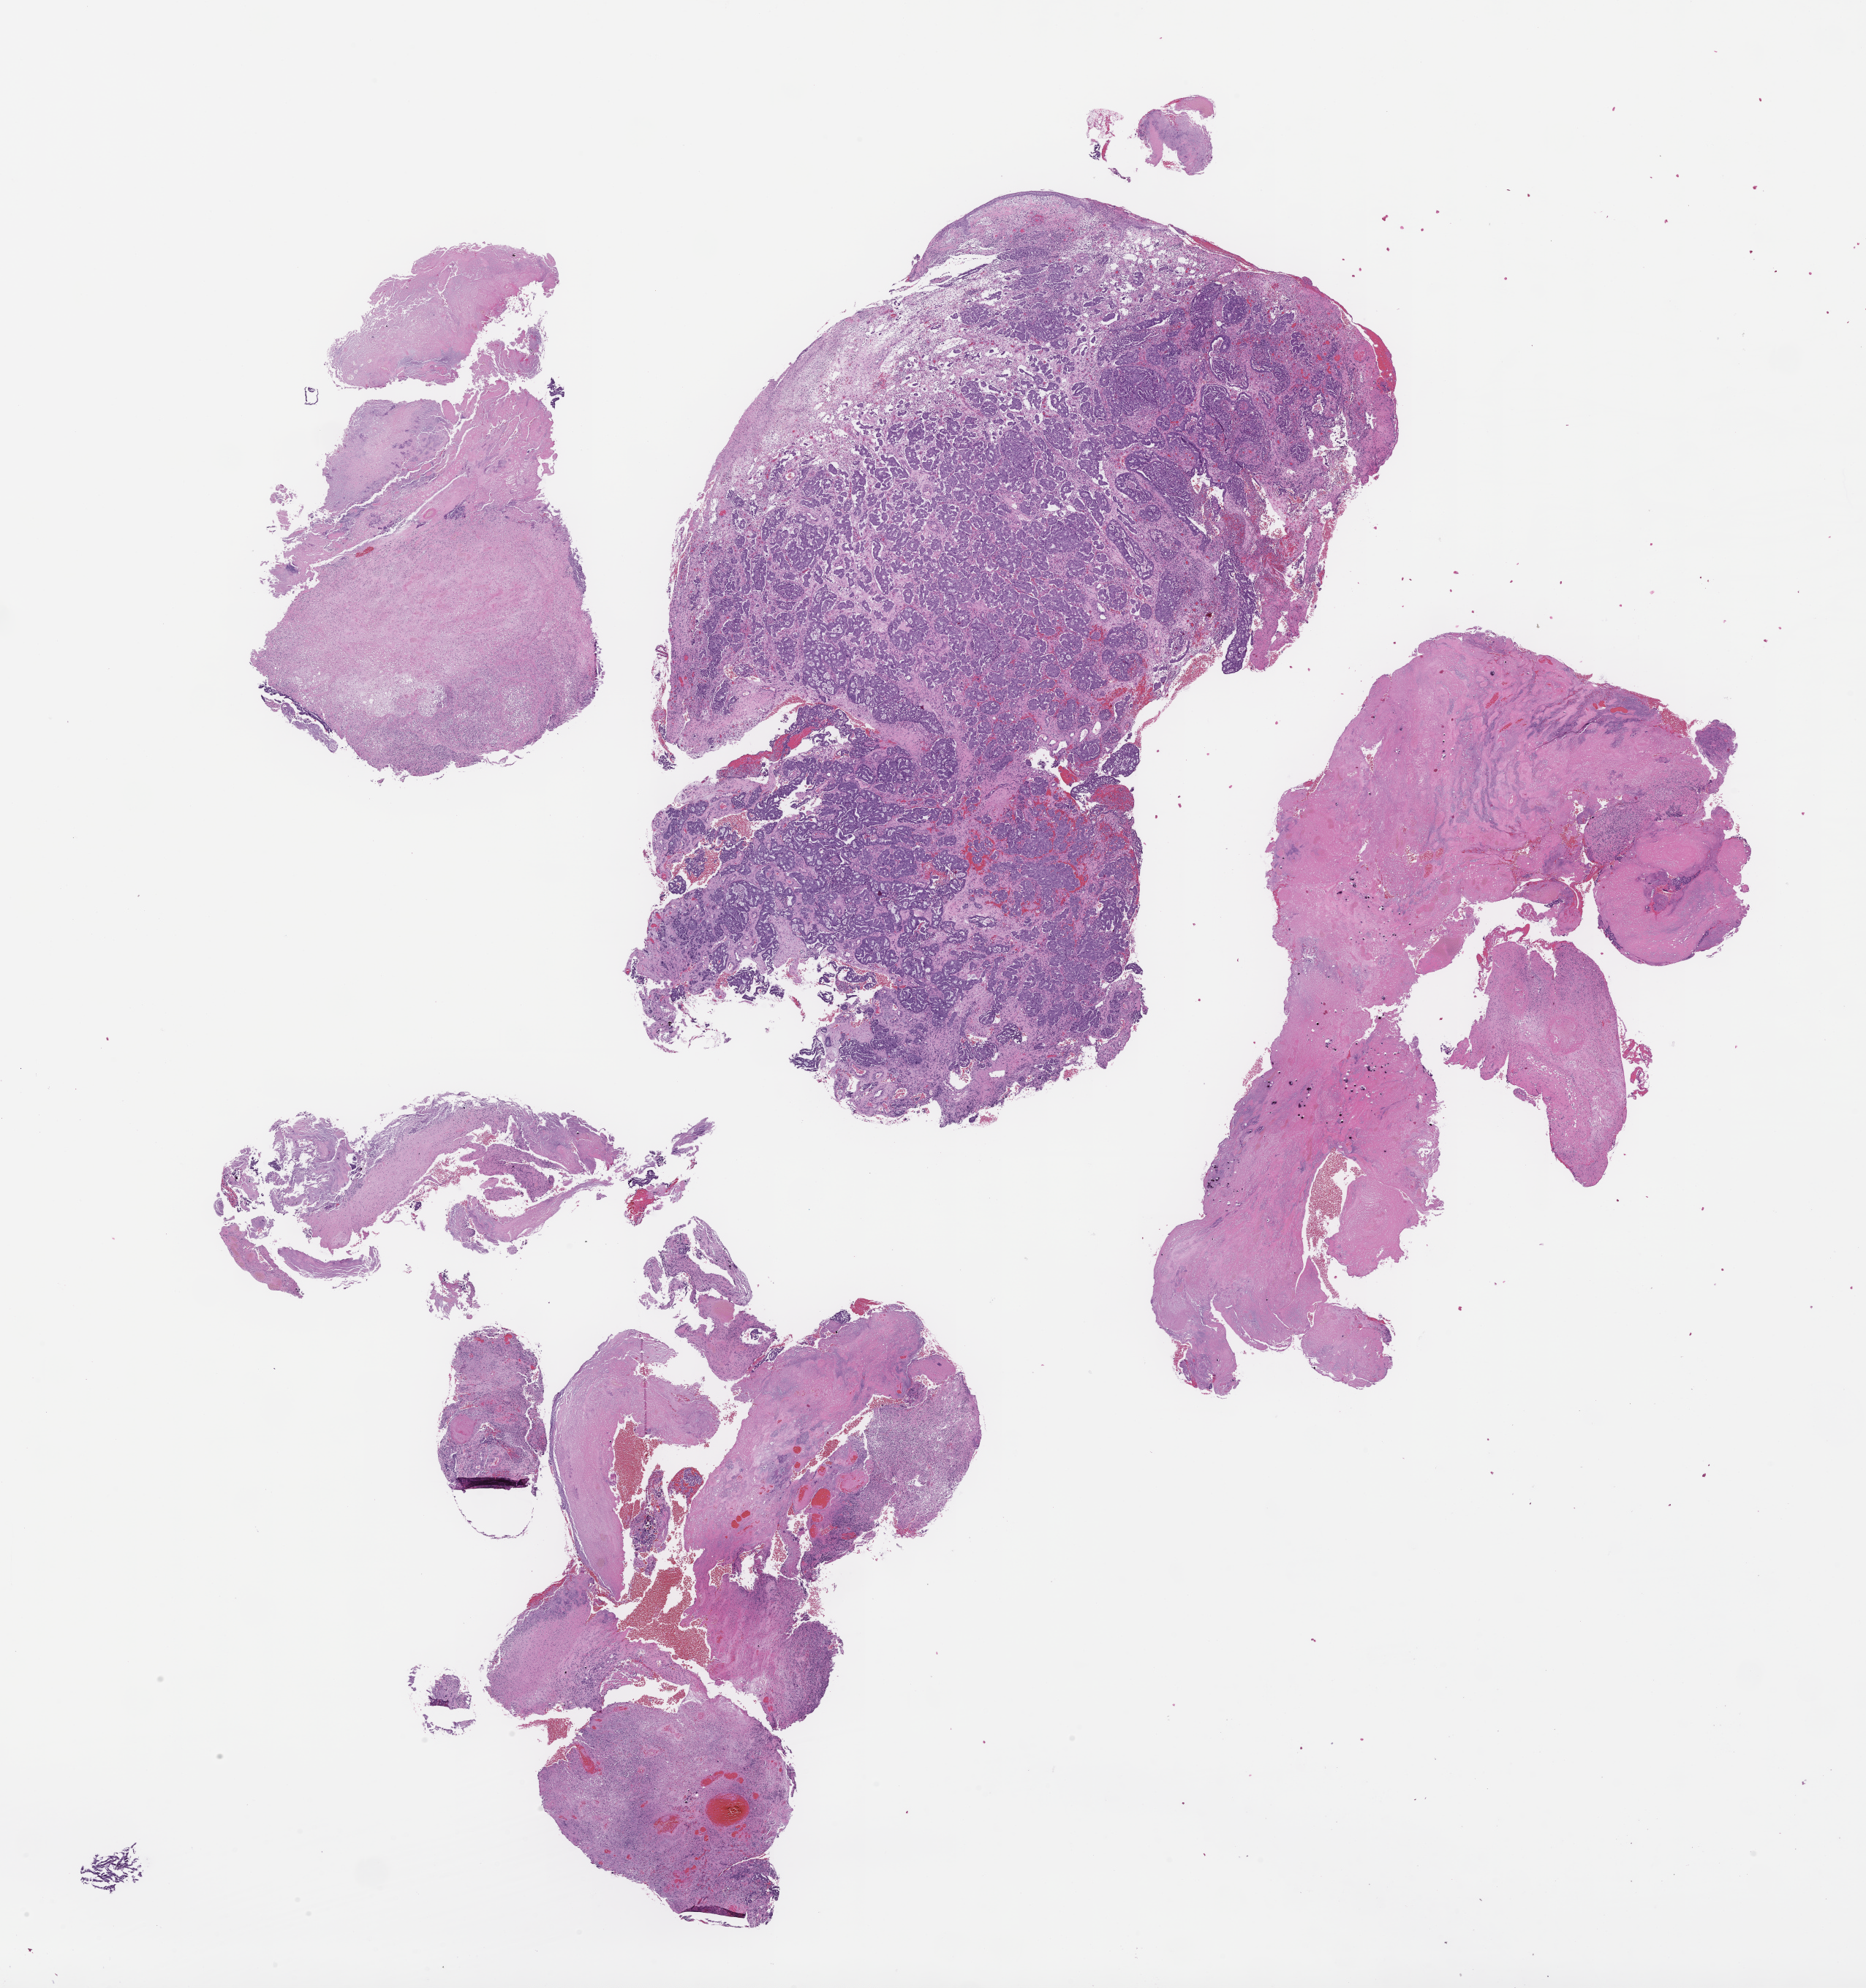
H&E whole-slide image, a low-resolution overview of the entire scanned area, about 20.6 x 22.0 mm. Formalin-fixed, paraffin-embedded (FFPE) tissue. Specimen time point: archival tissue. Patient: female.
This section: metastasis (sampled organ not recorded). Patient diagnosis (primary): Ovarian Carcinoma.